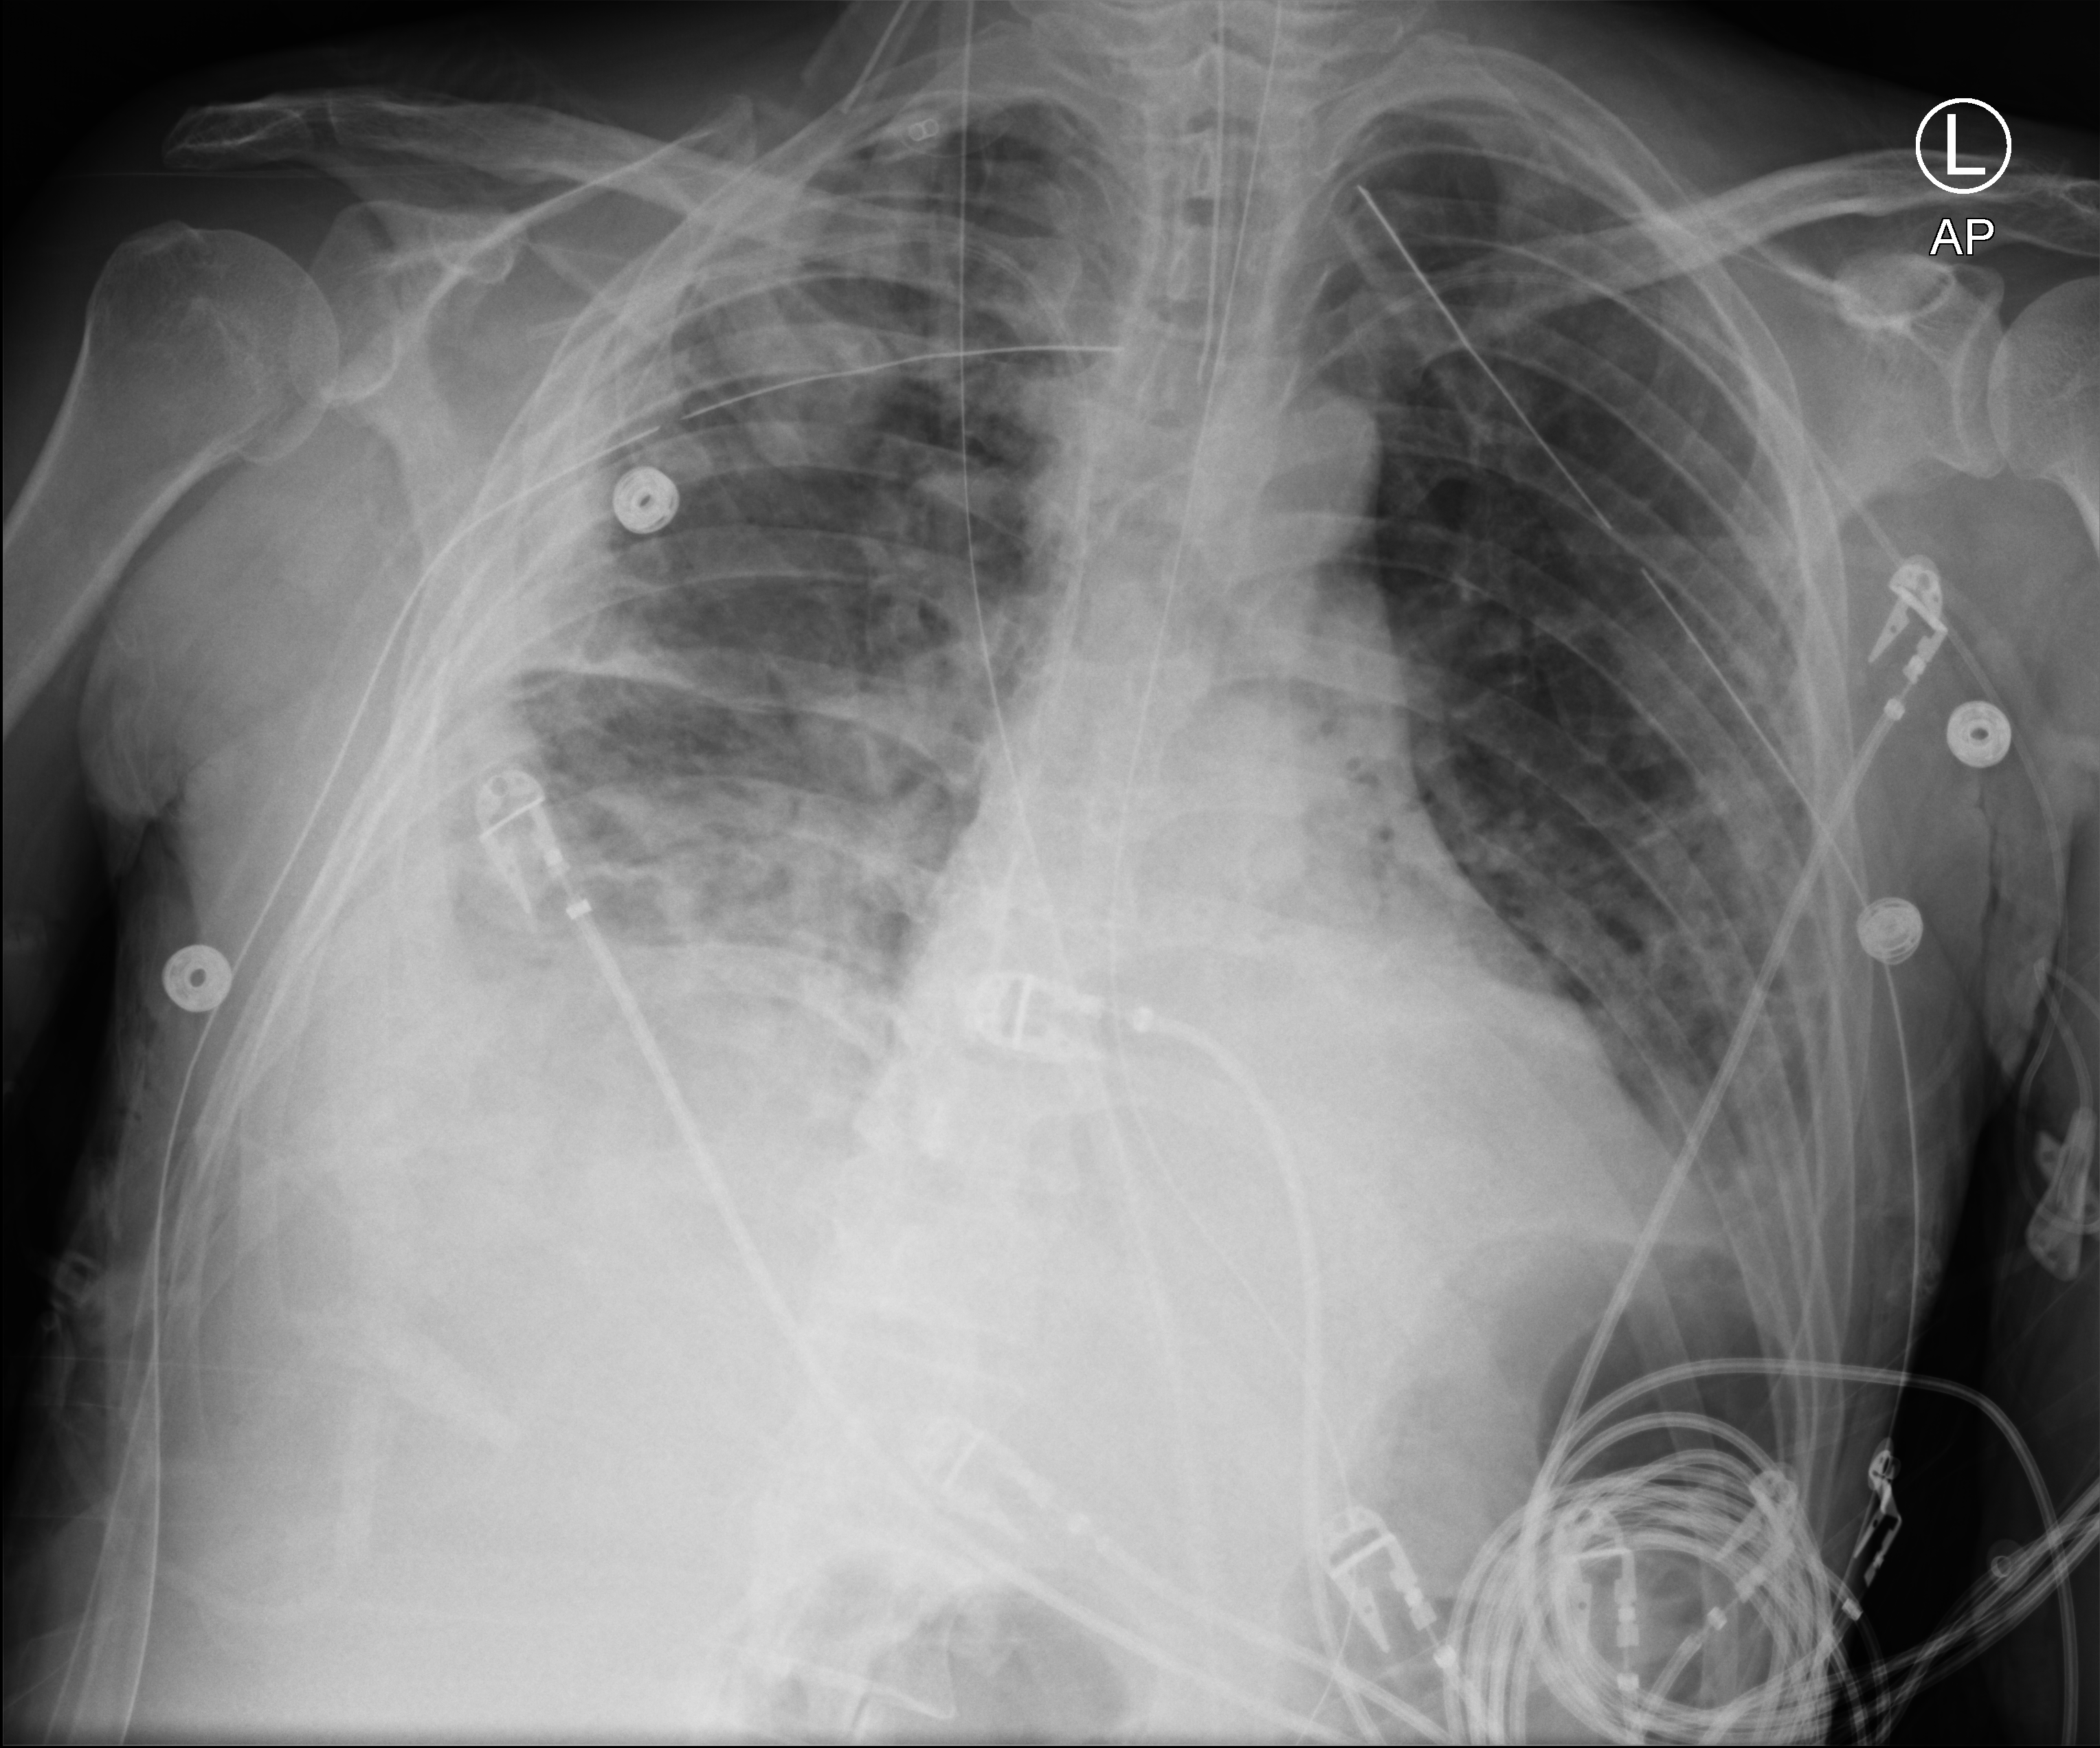
Portable chest radiograph. Patient hospitalised with COVID-19; male, aged 18–59 years.
From the hospital-stay record, not from the radiograph (when in the stay this image was taken is not recorded):
- other chronic lung disease (admission record): no
- diabetes (admission record): yes
- smoking status (admission record): never